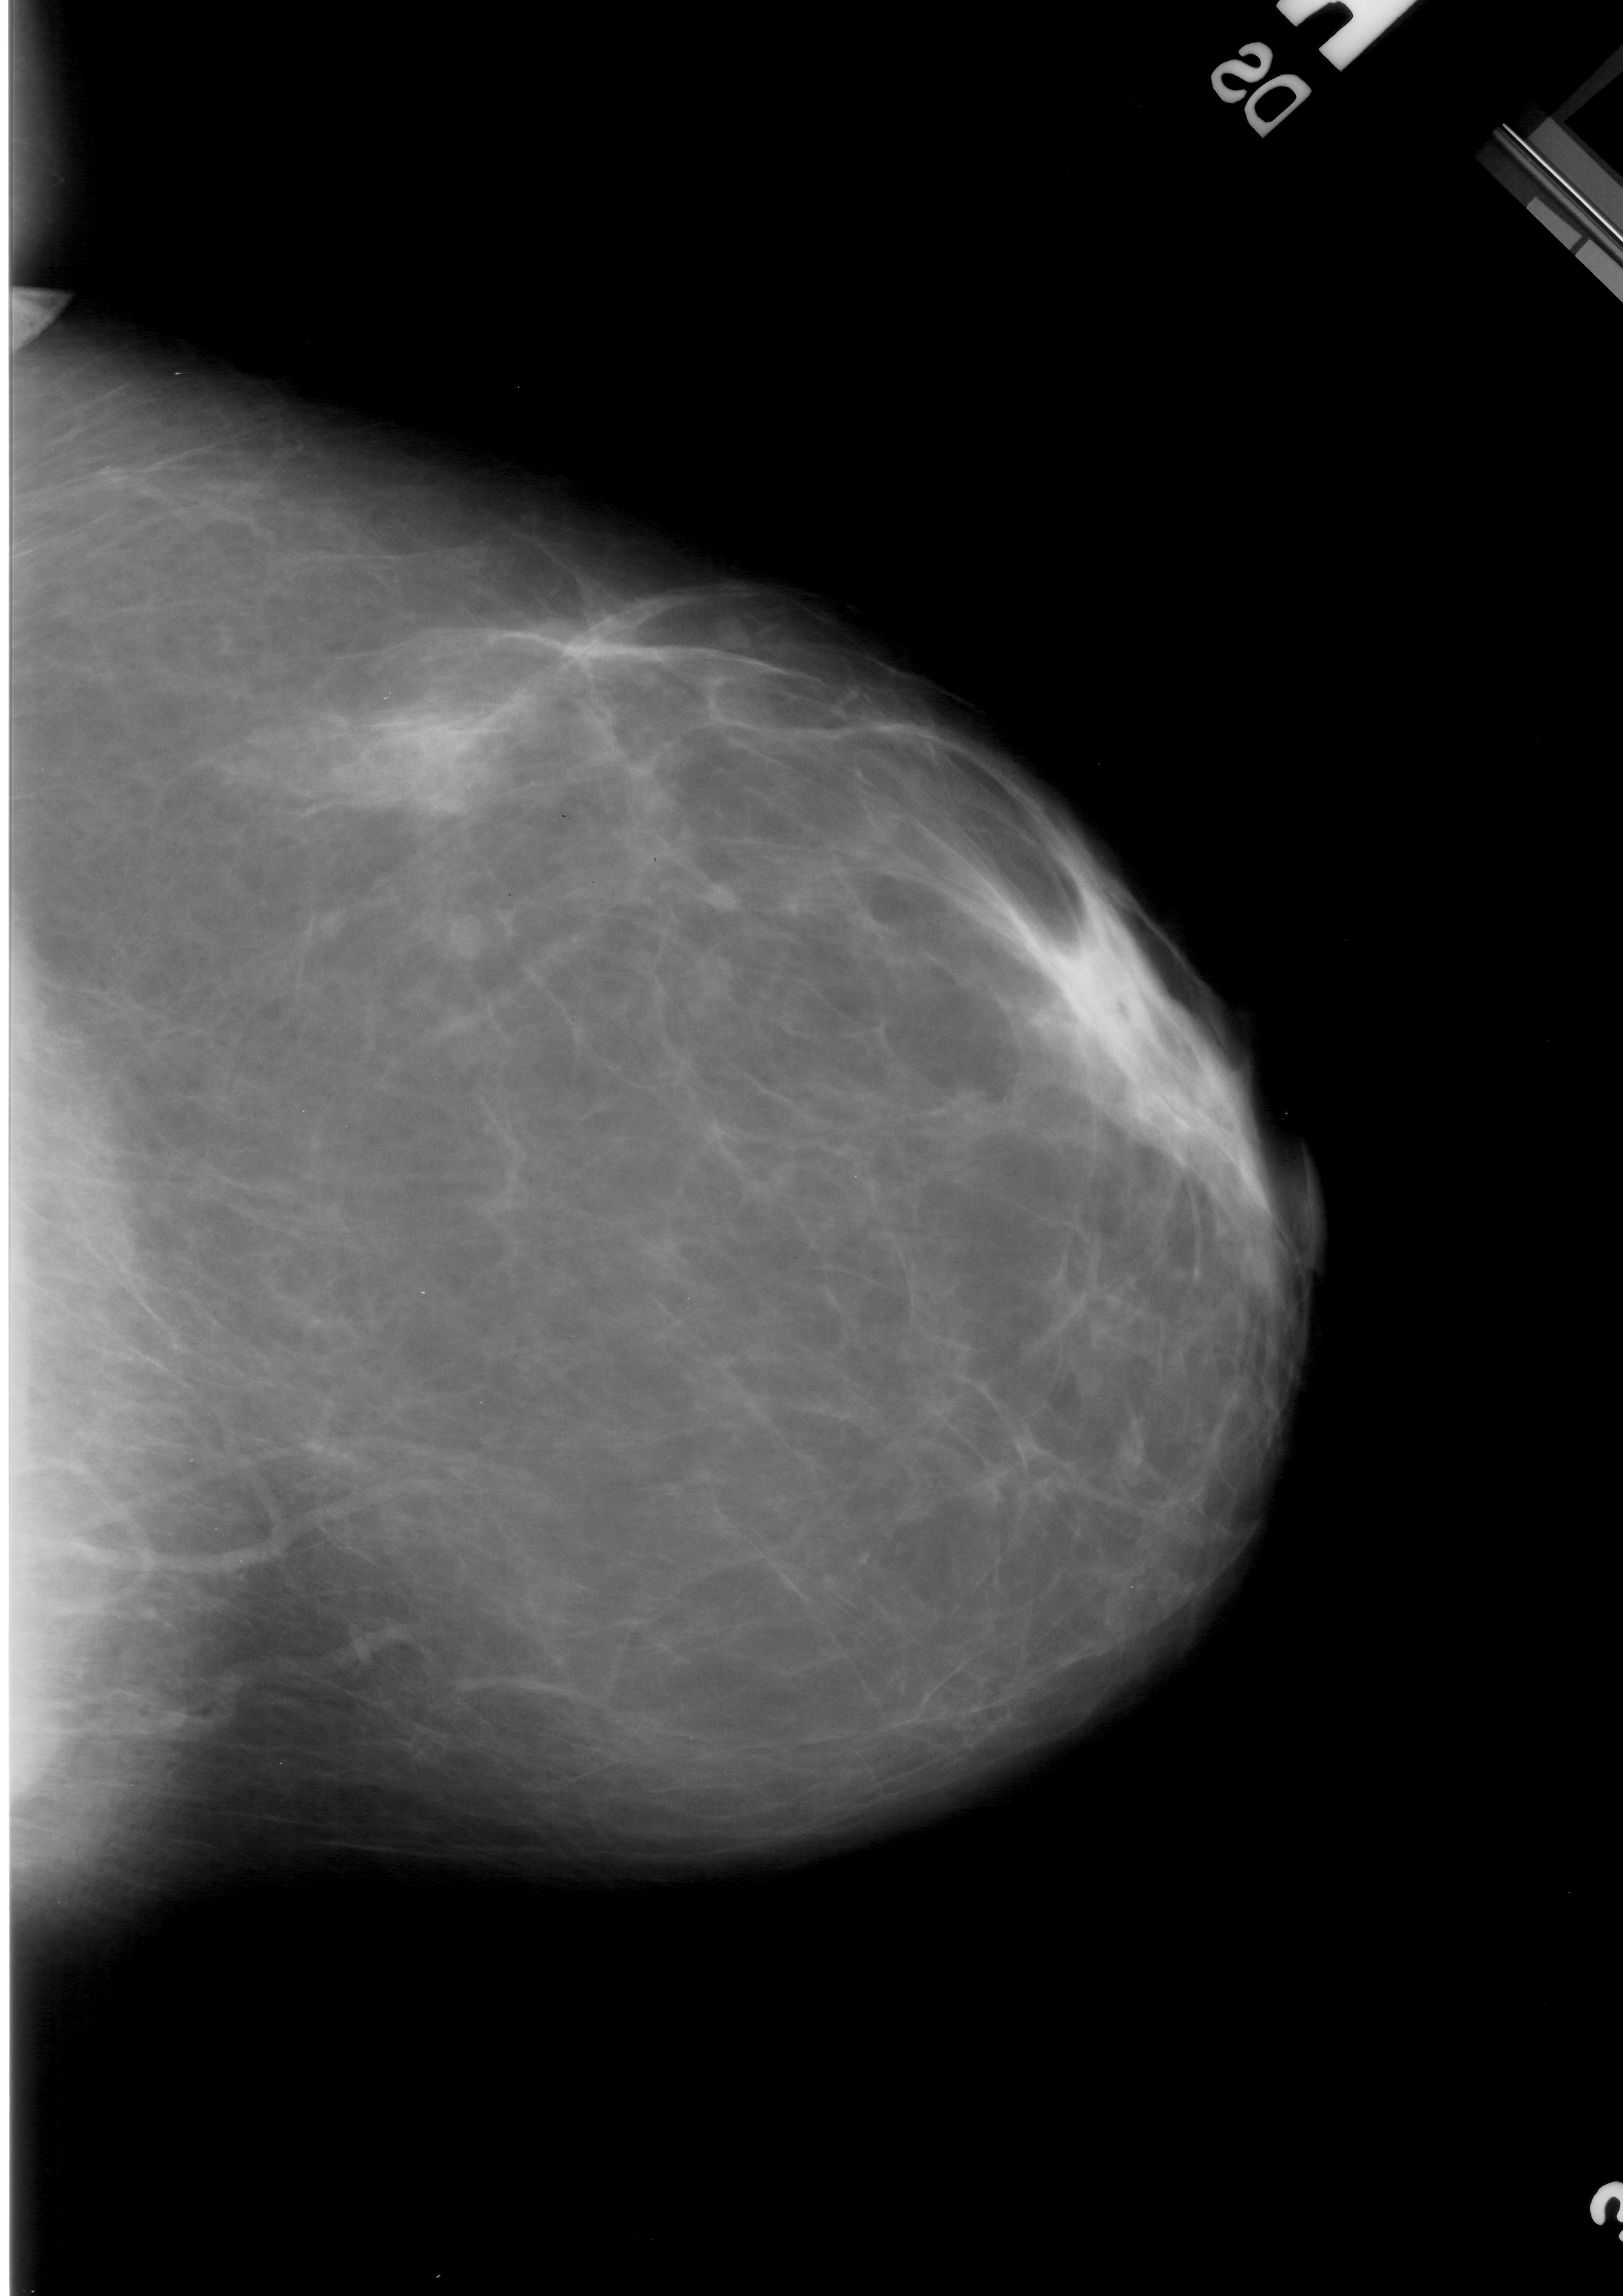
Mammogram (digitized film). Right breast. CC view. BI-RADS breast density category 1 (scale 1–4). 1623 × 2296 image matrix.
Marked abnormalities (boxes around the expert regions of interest):
- mass, shape lobulated, margins obscured; BI-RADS assessment category 3; pathology result (as recorded, not read from the image): benign: bounding box (x1, y1, x2, y2) in pixels: (374, 685, 516, 778)